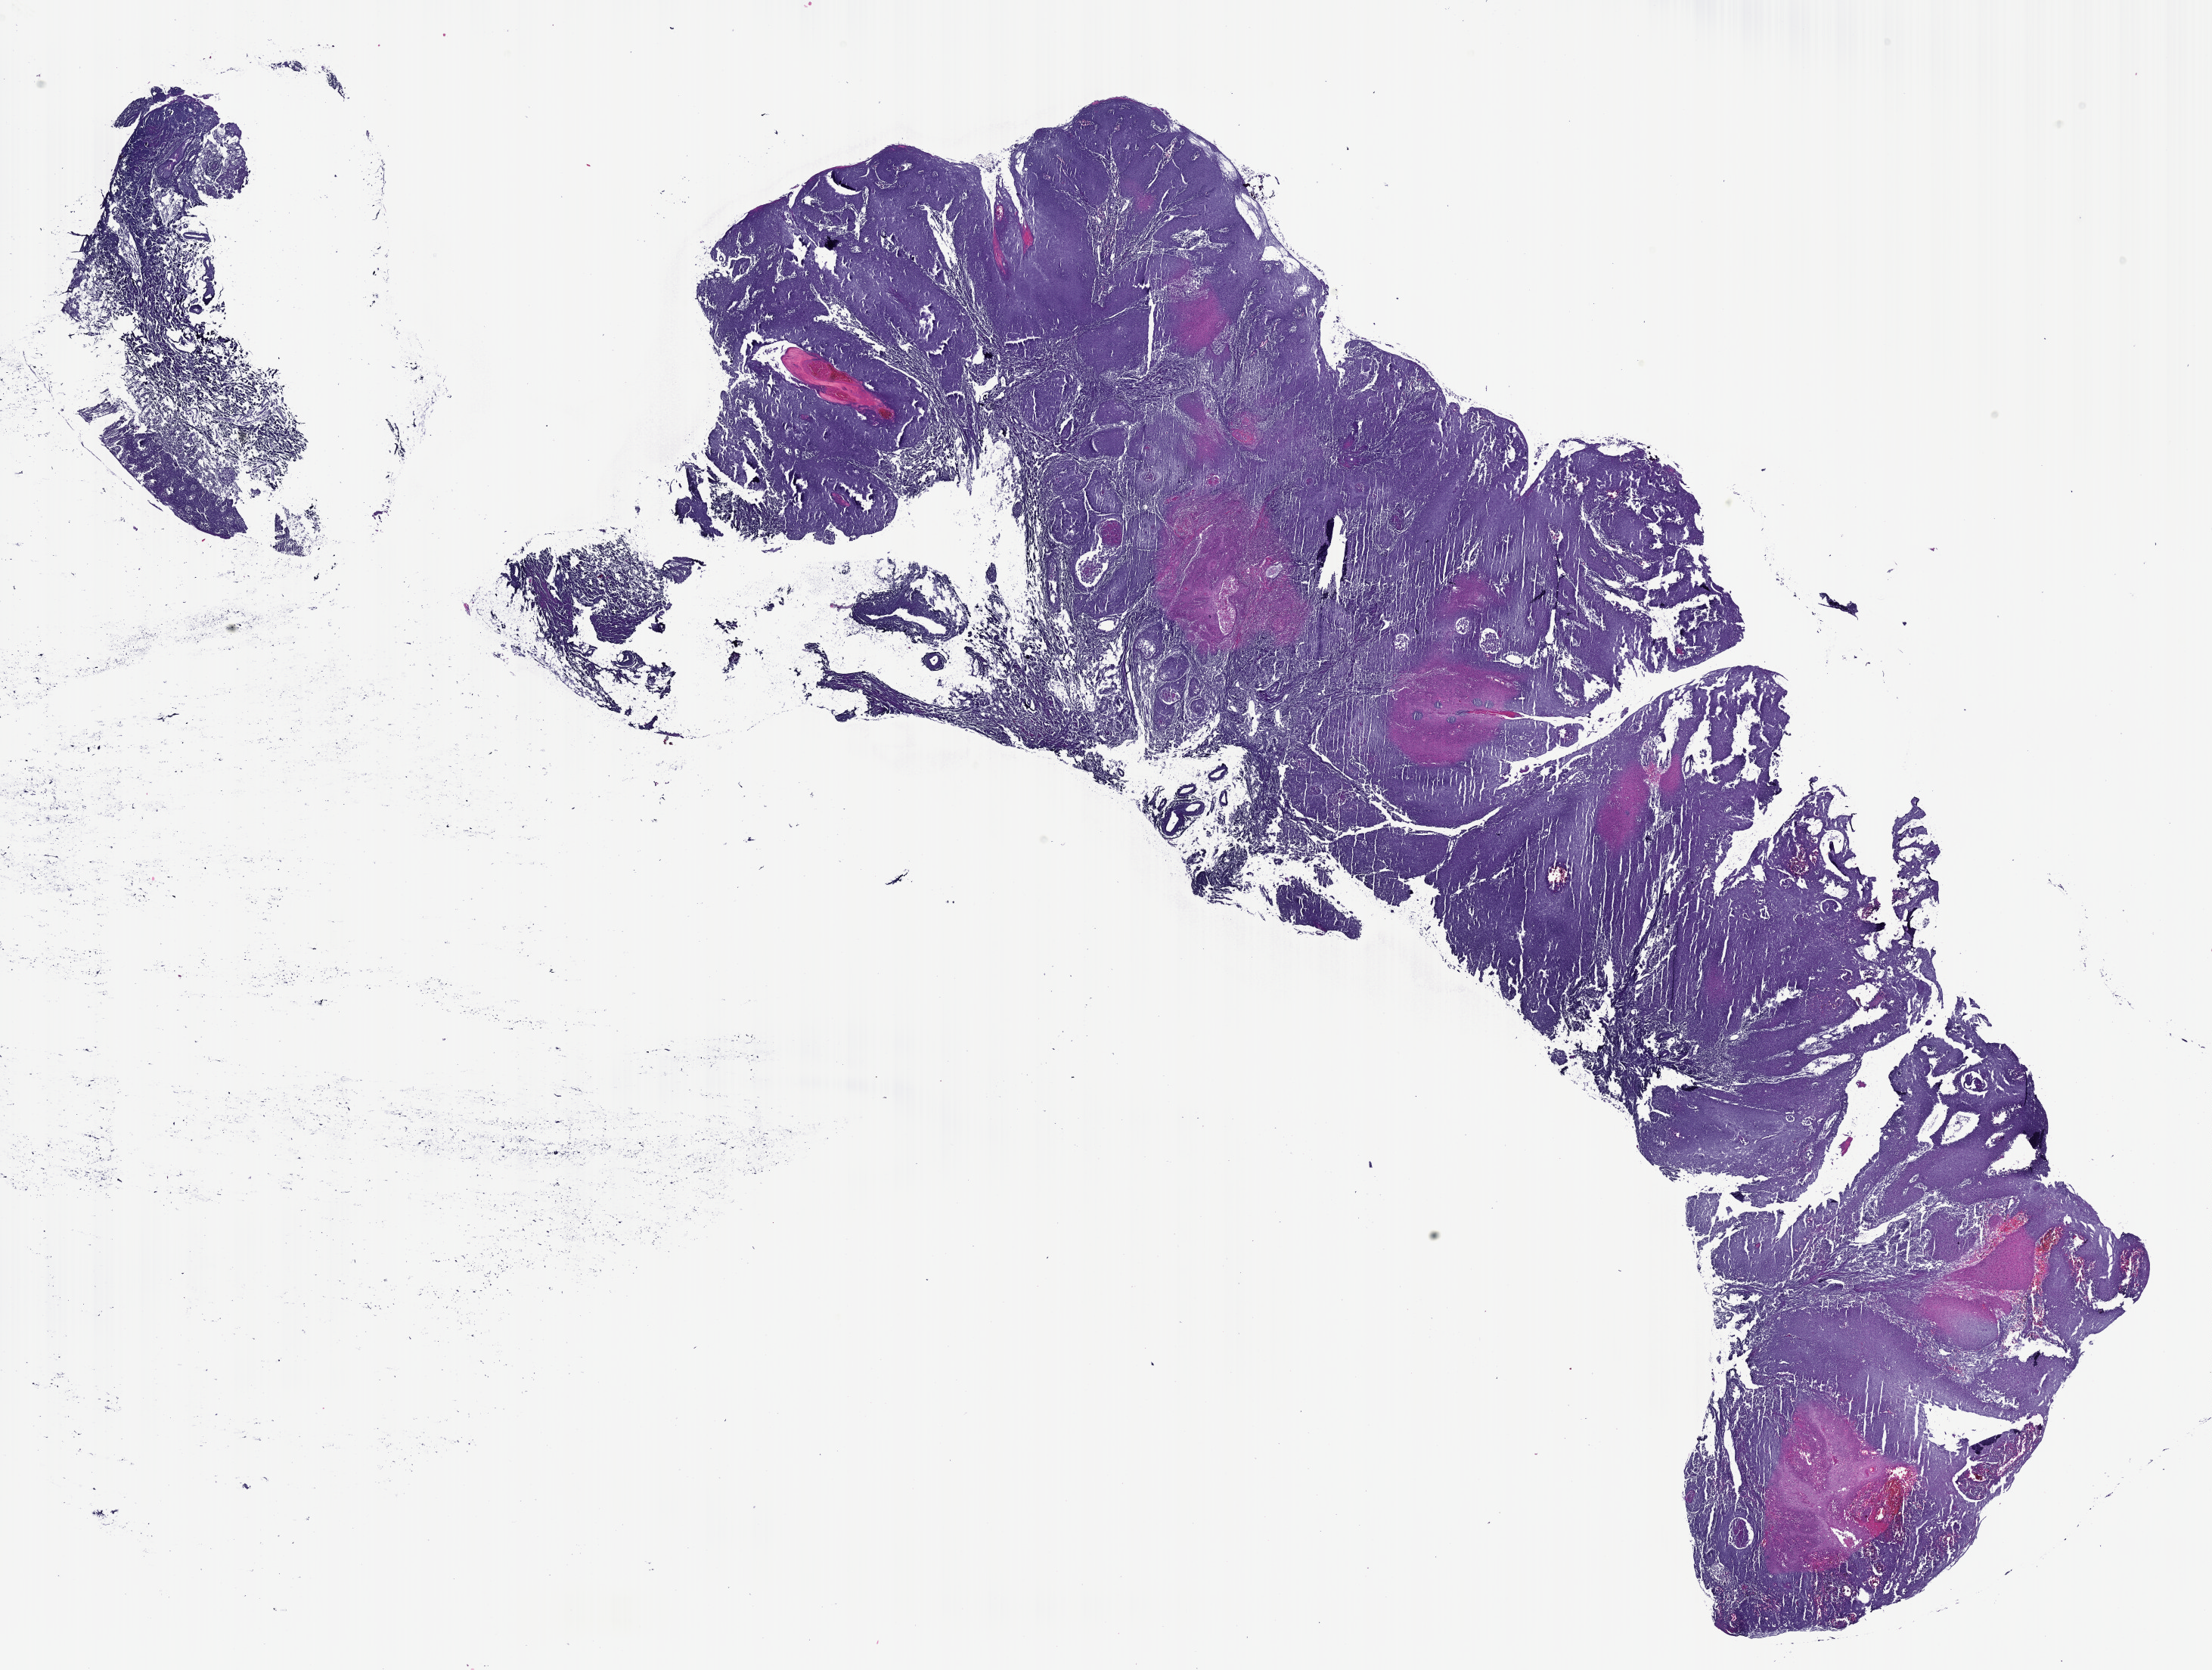
H&E-stained whole-slide image — shown as a low-resolution overview of the whole scanned area (about 23.6 x 17.8 mm). Formalin-fixed paraffin-embedded (FFPE) diagnostic section. Head and neck, primary tumour sample. Female, age 73 years at initial diagnosis. Histologic grade: G1 (well differentiated).
AJCC pathologic stage: II. Laterality: right. Histologic diagnosis: Squamous cell carcinoma, NOS (overlapping lesion of lip, oral cavity and pharynx).